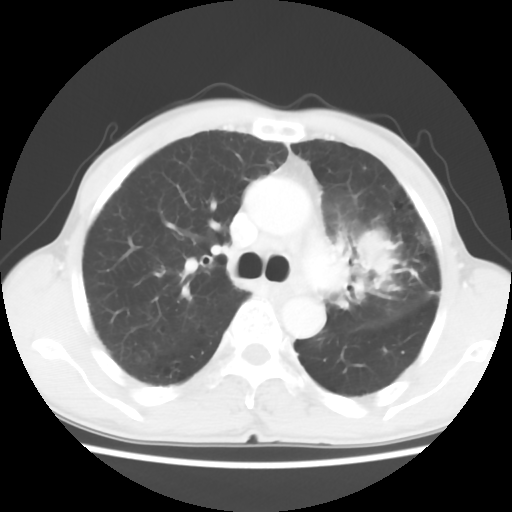
Chest CT, one axial slice. Position 39 of 60 along the scan axis. Reconstruction kernel STANDARD. 120 kVp. Lung window (W 1500 / L -600 HU). 5 mm slice thickness. 512 × 512 image matrix, field of view 308 × 308 mm. Patient: male, 64 years. Case-level facts recorded for this patient, not image findings: clinical TNM (as recorded): T3 N3 M0; histopathological grade: G3.
Structures marked on this image (bounding box drawn by a radiologist):
- lung tumour (recorded histology: adenocarcinoma): bounding box <331,202,410,315> (left, top, right, bottom; pixels)